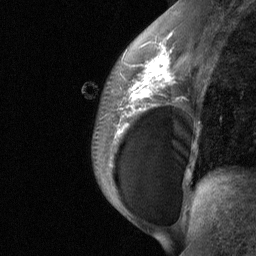
Breast MRI (dynamic contrast-enhanced), one sagittal slice. Slice 40 of 64 in the series (ordered by position). Dynamic contrast-enhanced study with each time point stored as its own series, time point 2 of 3 at this slice position (early post-contrast, ordered by acquisition time). 1.5 T. TE 4.8 ms, TR 27 ms. 2 mm slice thickness. 256 × 256 image matrix, field of view 200 × 200 mm. Female patient, age 34 years. Case-level facts recorded for this patient, not image findings: setting: breast cancer imaged before/during neoadjuvant chemotherapy; receptor status: HR-positive, HER2-negative.
Outlined on this slice (semi-automatically segmented with operator editing):
- analysis volume of interest (the breast-tissue region the enhancement analysis was run in; not a lesion): box from (x=92, y=50) to (x=188, y=185) px
- tumour enhancement mask (voxels above the 90 % enhancement threshold inside the analysis volume of interest): (x=118, y=50)–(x=174, y=132)